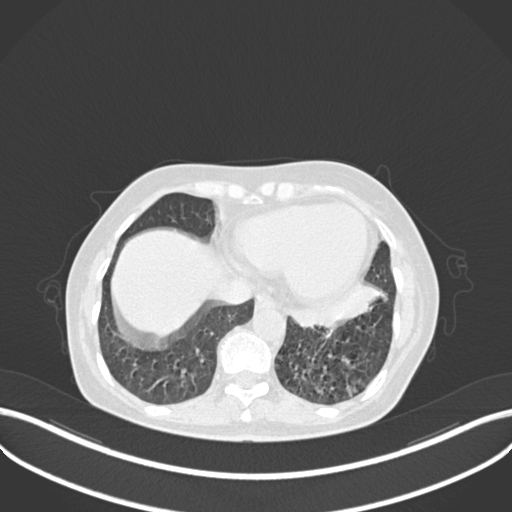
Chest CT, one axial slice; position 68 of 270 along the scan axis; reconstruction kernel B30f; lung window (W 1500 / L -600 HU); 512 × 512 image matrix, field of view 400 × 400 mm. Female patient, age 63 years. Case-level facts recorded for this patient, not image findings: clinical TNM (as recorded): T1b N0 M0.
Outlined on this slice (rectangle marked by the reading radiologist):
- lung tumour (recorded histology: adenocarcinoma): bounding box (x1, y1, x2, y2) in pixels: (282, 280, 391, 334)